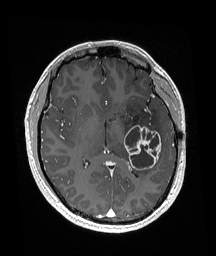
Brain MRI from a brain-tumour surgery series, one axial slice. Slice 93 of 192 in the series (ordered by position). T1-weighted post-contrast. 1 mm slice thickness. 216 × 256 image matrix. From the clinical record (not read from this slice): histopathology: Glioneuronal tumor; WHO grade: 2.
Outlined on this slice (outlined manually by an expert reader):
- tumour: bounding box [x1, y1, x2, y2] px = [124, 125, 162, 171]